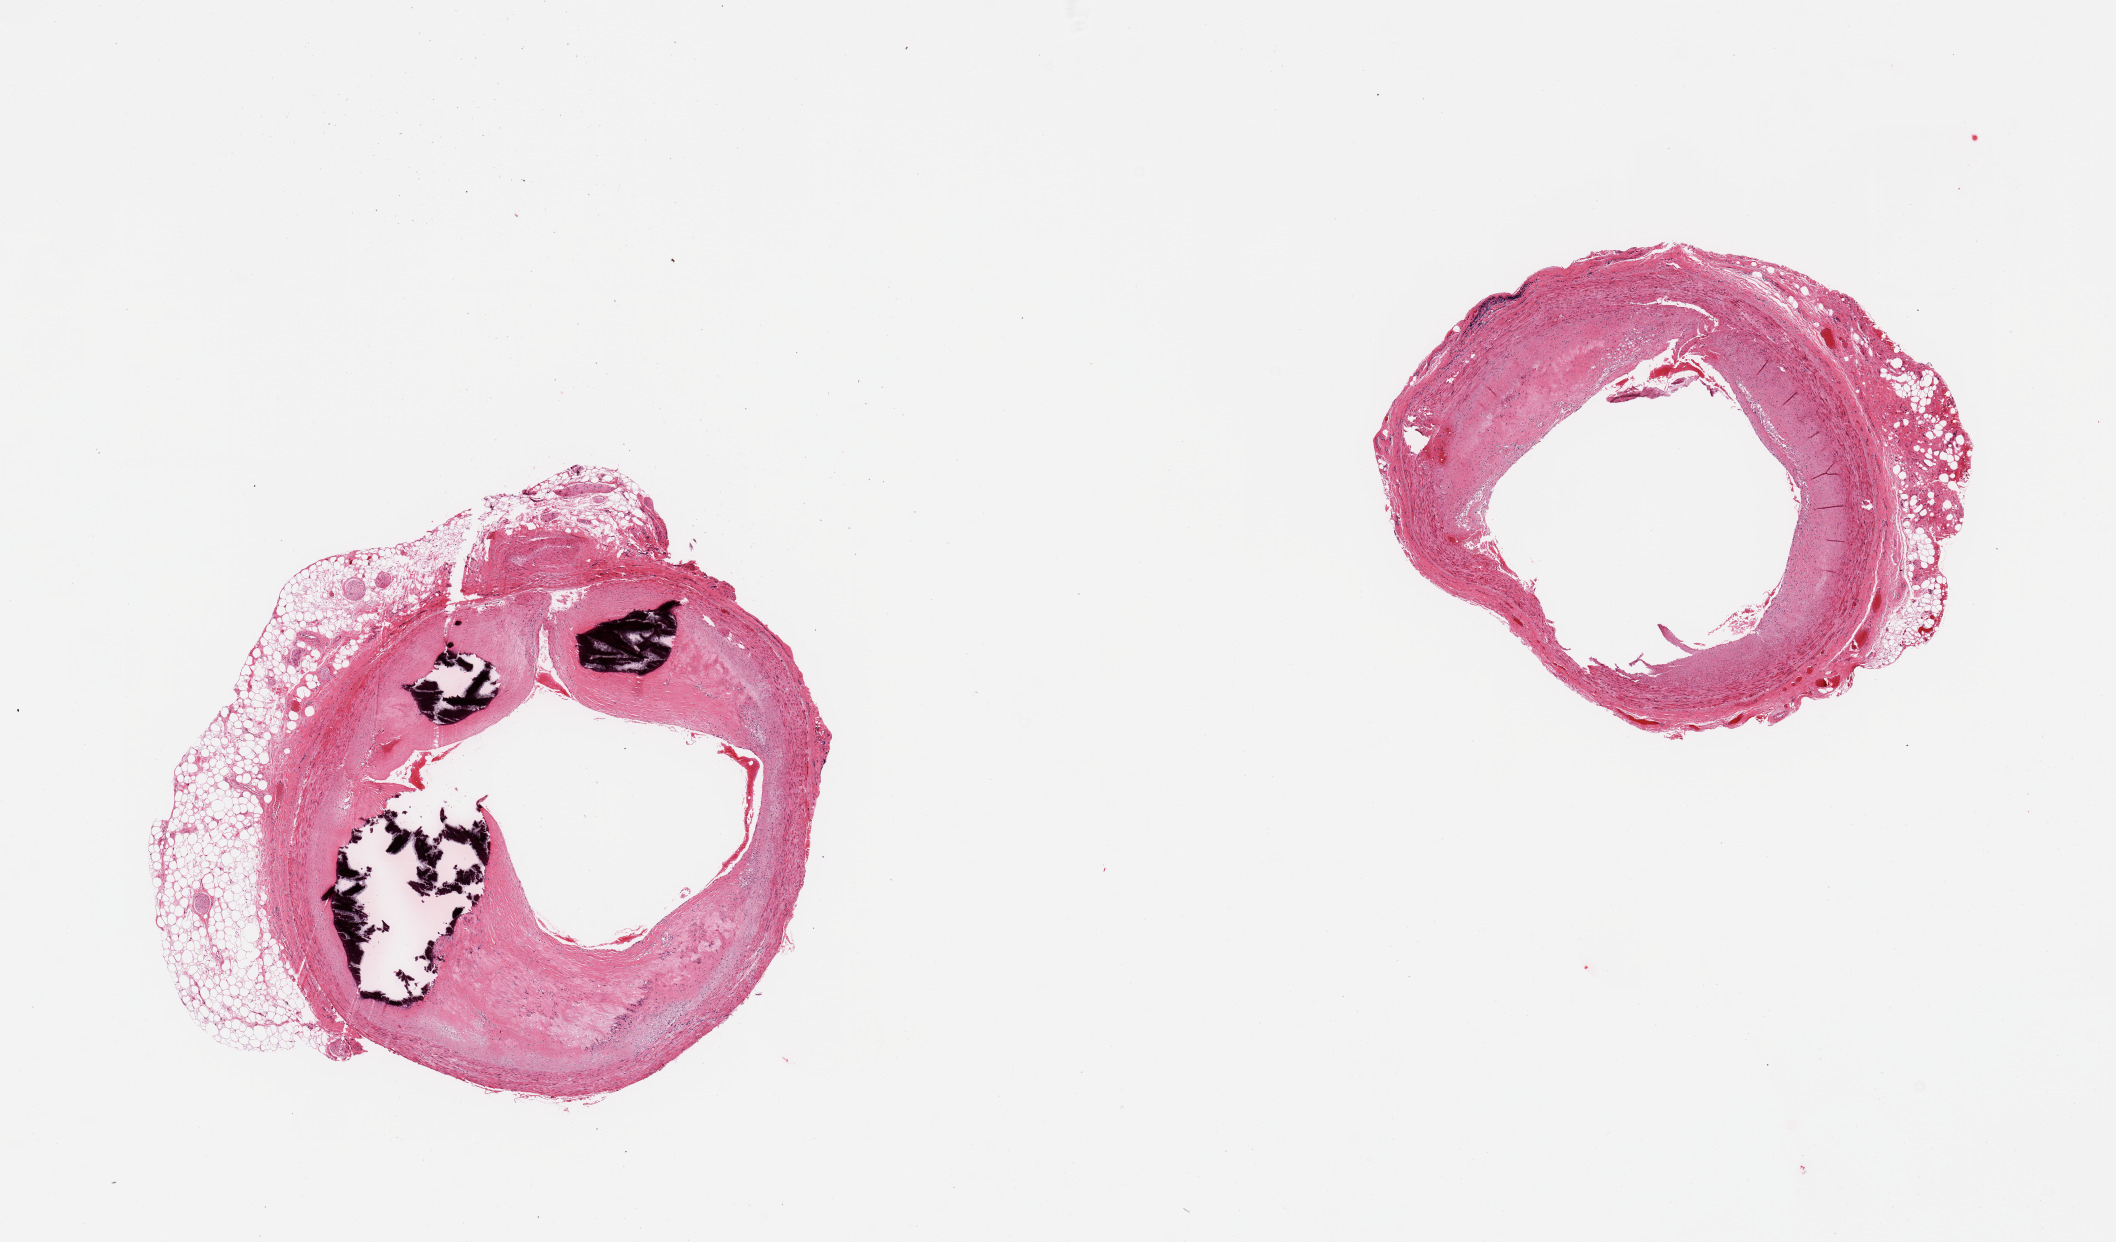
Digitized H&E-stained section — whole scanned area (about 16.7 x 9.8 mm, from a 20x scan) shown as a low-resolution overview, PAXgene-fixed, paraffin-embedded tissue, section of coronary artery (target tissue), donor tissue sample. Donor: male.
Review note (as recorded): 2 pieces, ~60% occlusive calcifying atherosis; adherent rim of fat up to ~0.6mm.